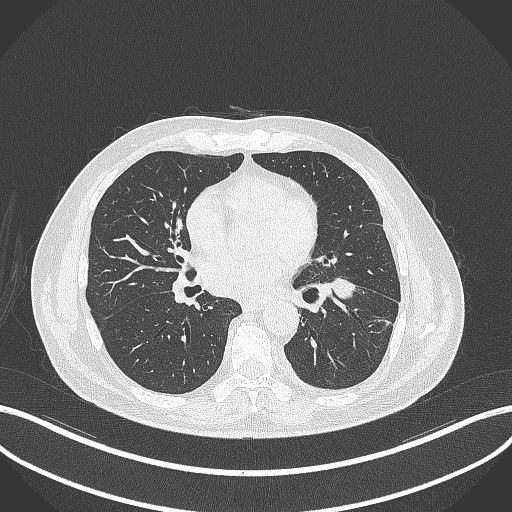
Chest CT, one axial slice; position 171 of 230 along the scan axis; reconstruction kernel B70f; 120 kVp; lung window (W 1500 / L -600 HU); 512 × 512 image matrix, field of view 400 × 400 mm. Male patient, age 68 years. Case-level facts recorded for this patient, not image findings: clinical TNM (as recorded): T2b N0 M0.
Annotated regions visible in this slice (rectangle marked by the reading radiologist):
- lung tumour (recorded histology: squamous cell carcinoma): bounding box (x1, y1, x2, y2) in pixels: (327, 275, 360, 303)